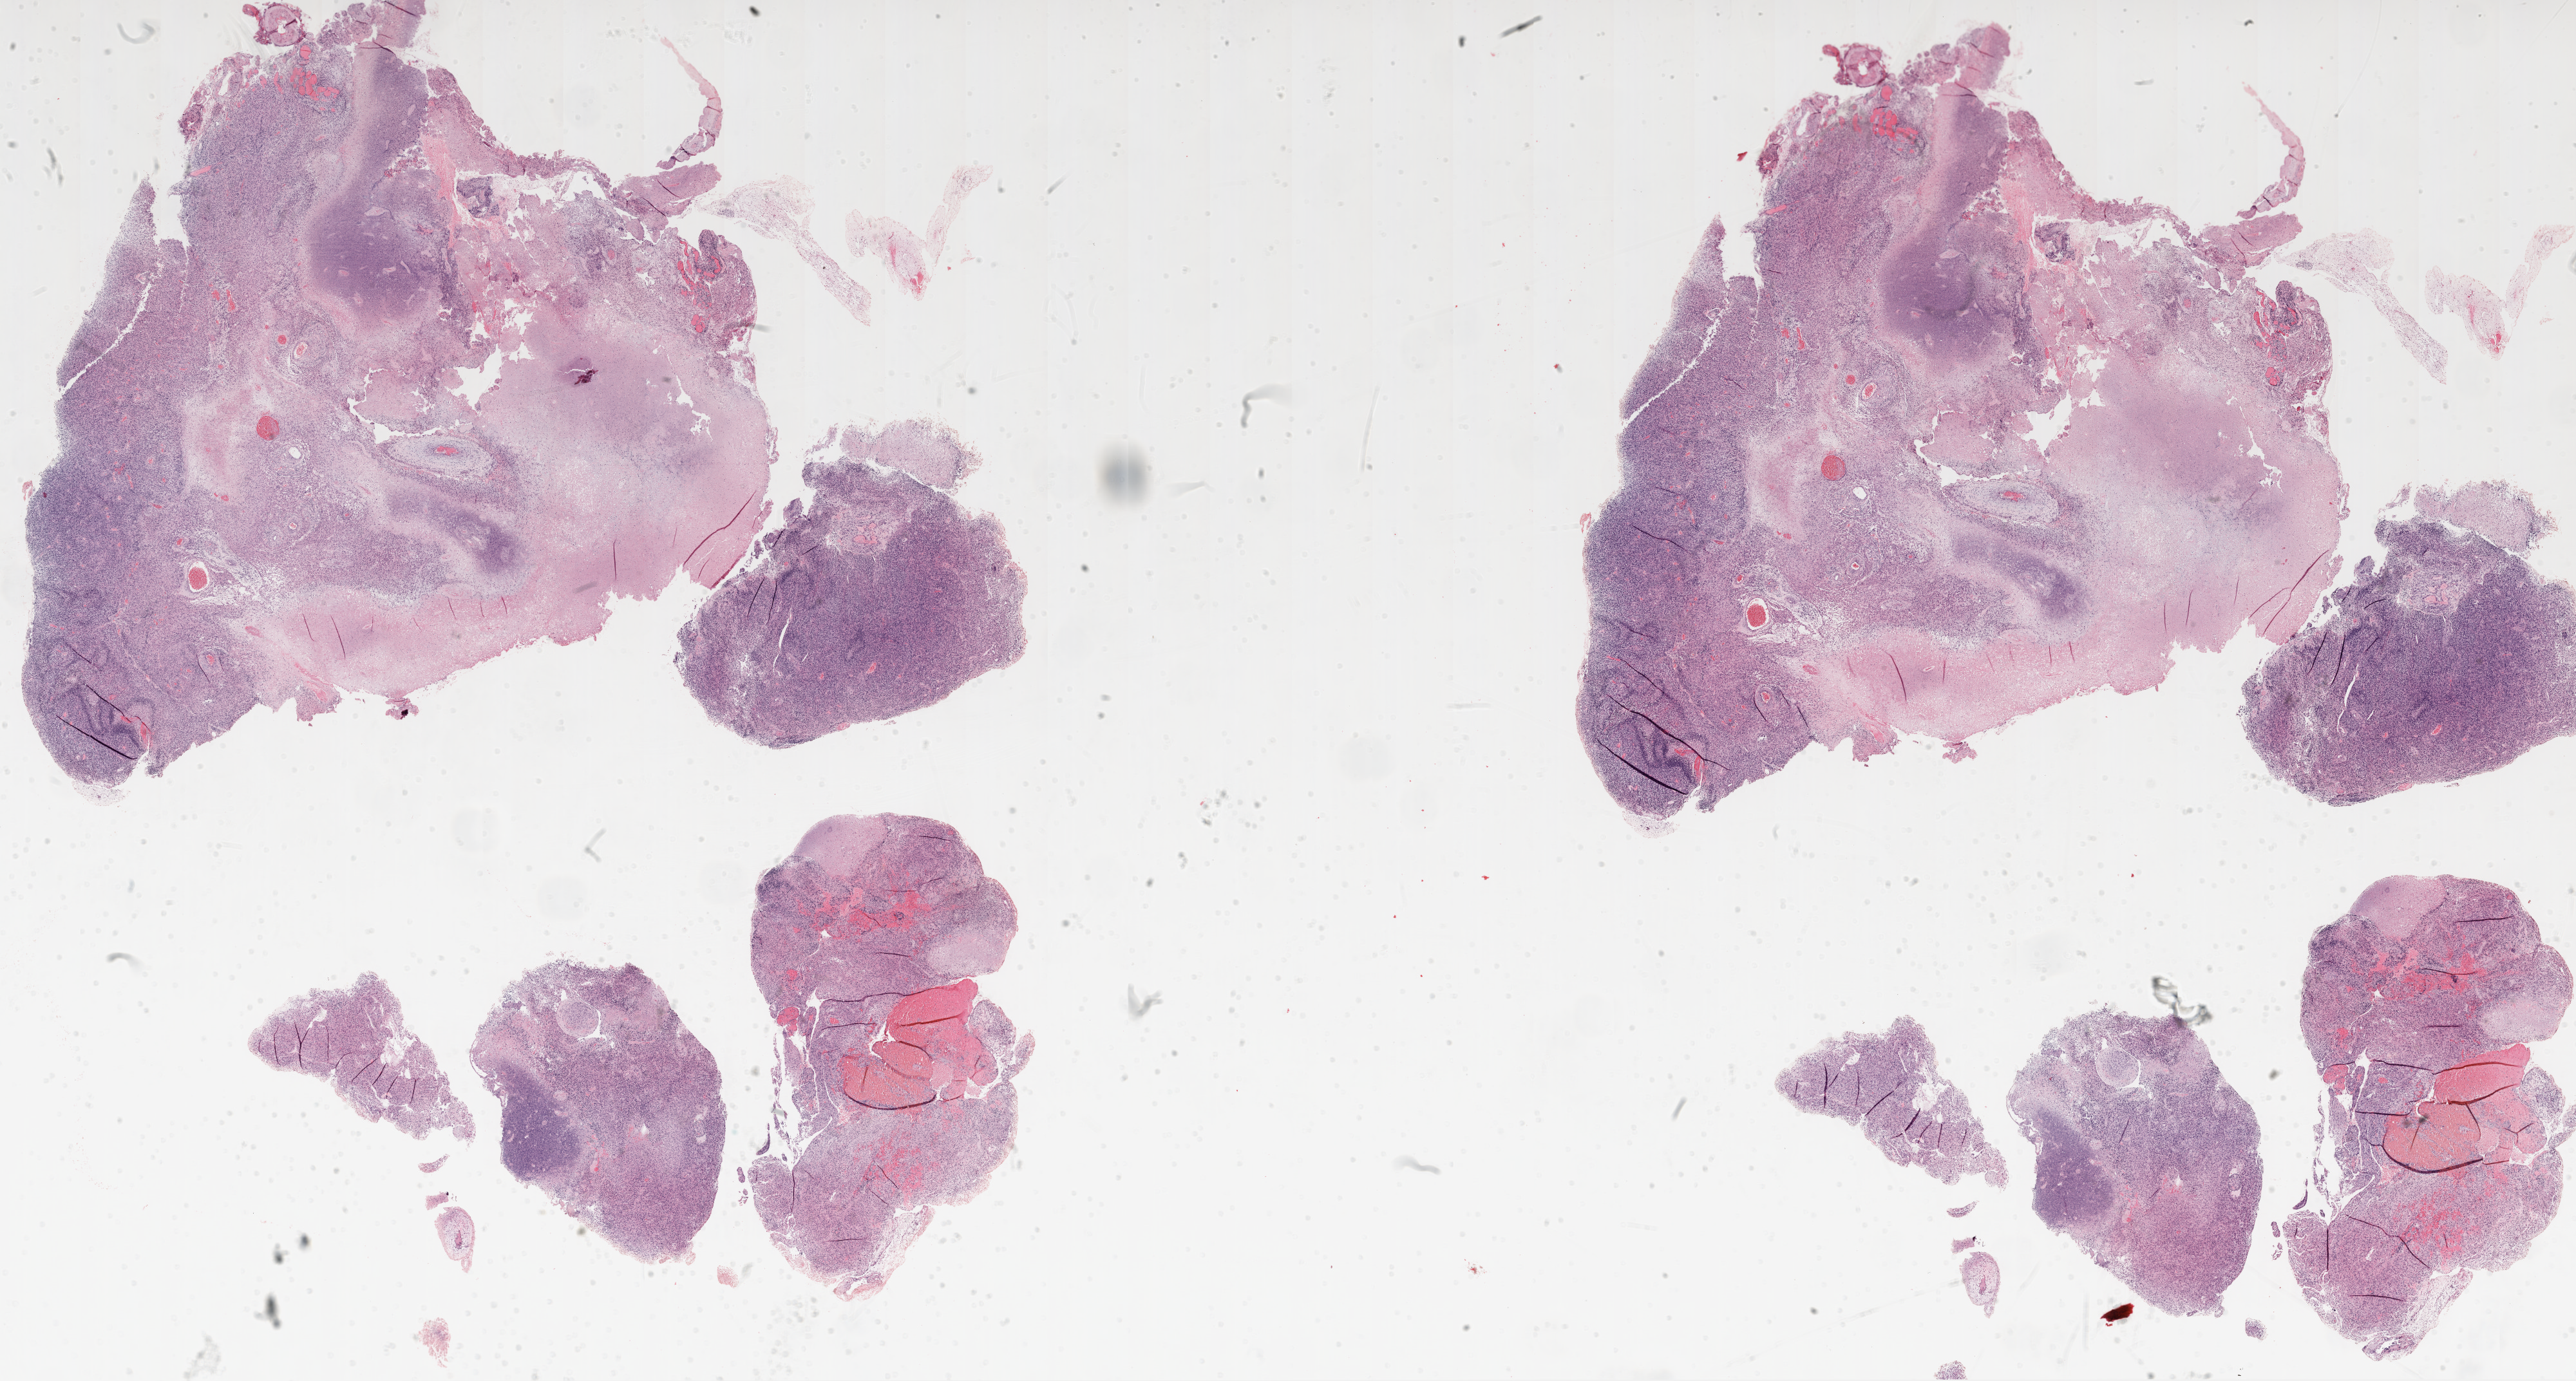
H&E-stained whole-slide image, whole scanned area (about 32.1 x 17.2 mm) shown as a low-resolution overview. Formalin-fixed paraffin-embedded (FFPE) diagnostic section. Sample: primary tumour, brain. Patient: female, age at initial diagnosis 66 years.
• pathologic diagnosis: Glioblastoma